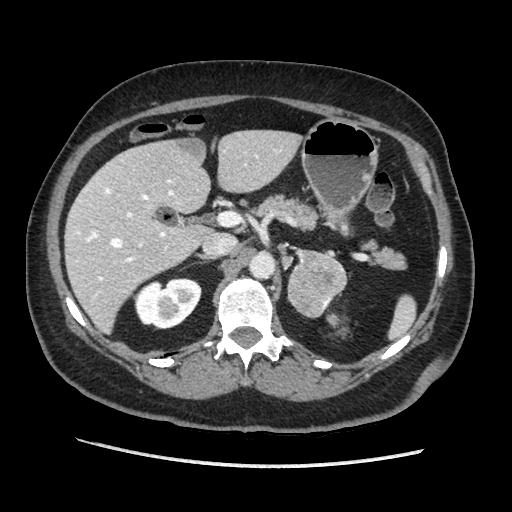
Contrast-enhanced abdominal CT, one axial slice. Position 119 of 203 along the scan axis. Soft-tissue window (W 400 / L 40 HU). 1.25 mm slice thickness. 512 × 512 image matrix, field of view 360 × 360 mm. Female patient. Case-level facts recorded for this patient, not image findings: diagnosis: adrenocortical carcinoma; tumour side: left adrenal; tumour size at pathology: 6.5 cm; Ki-67 index: 22 %; stage (as recorded): 2.
Structures marked on this image (semi-automatically segmented with operator editing):
- mass: box from (x=288, y=251) to (x=347, y=318) px